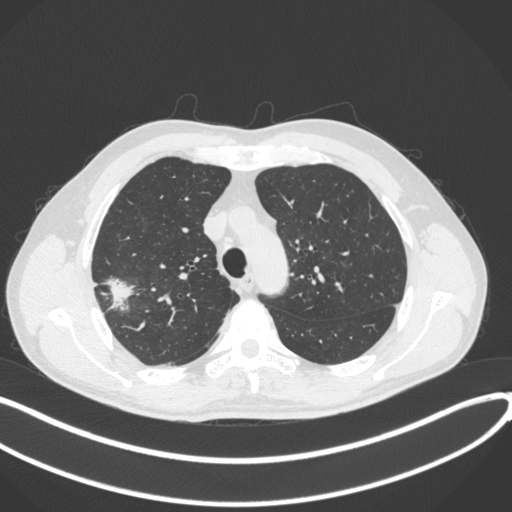
Chest CT, one axial slice; slice 314 of 381 in the series (ordered by position); lung window (W 1500 / L -600 HU); 1 mm slice thickness; 512 × 512 image matrix, field of view 400 × 400 mm. Male patient, age 62 years. Case-level facts recorded for this patient, not image findings: clinical TNM (as recorded): T1c N0 M0; histopathological grade: G2-3.
Structures marked on this image (rectangle marked by the reading radiologist):
- lung tumour (recorded histology: adenocarcinoma): bounding box [x1, y1, x2, y2] px = [99, 269, 140, 316]